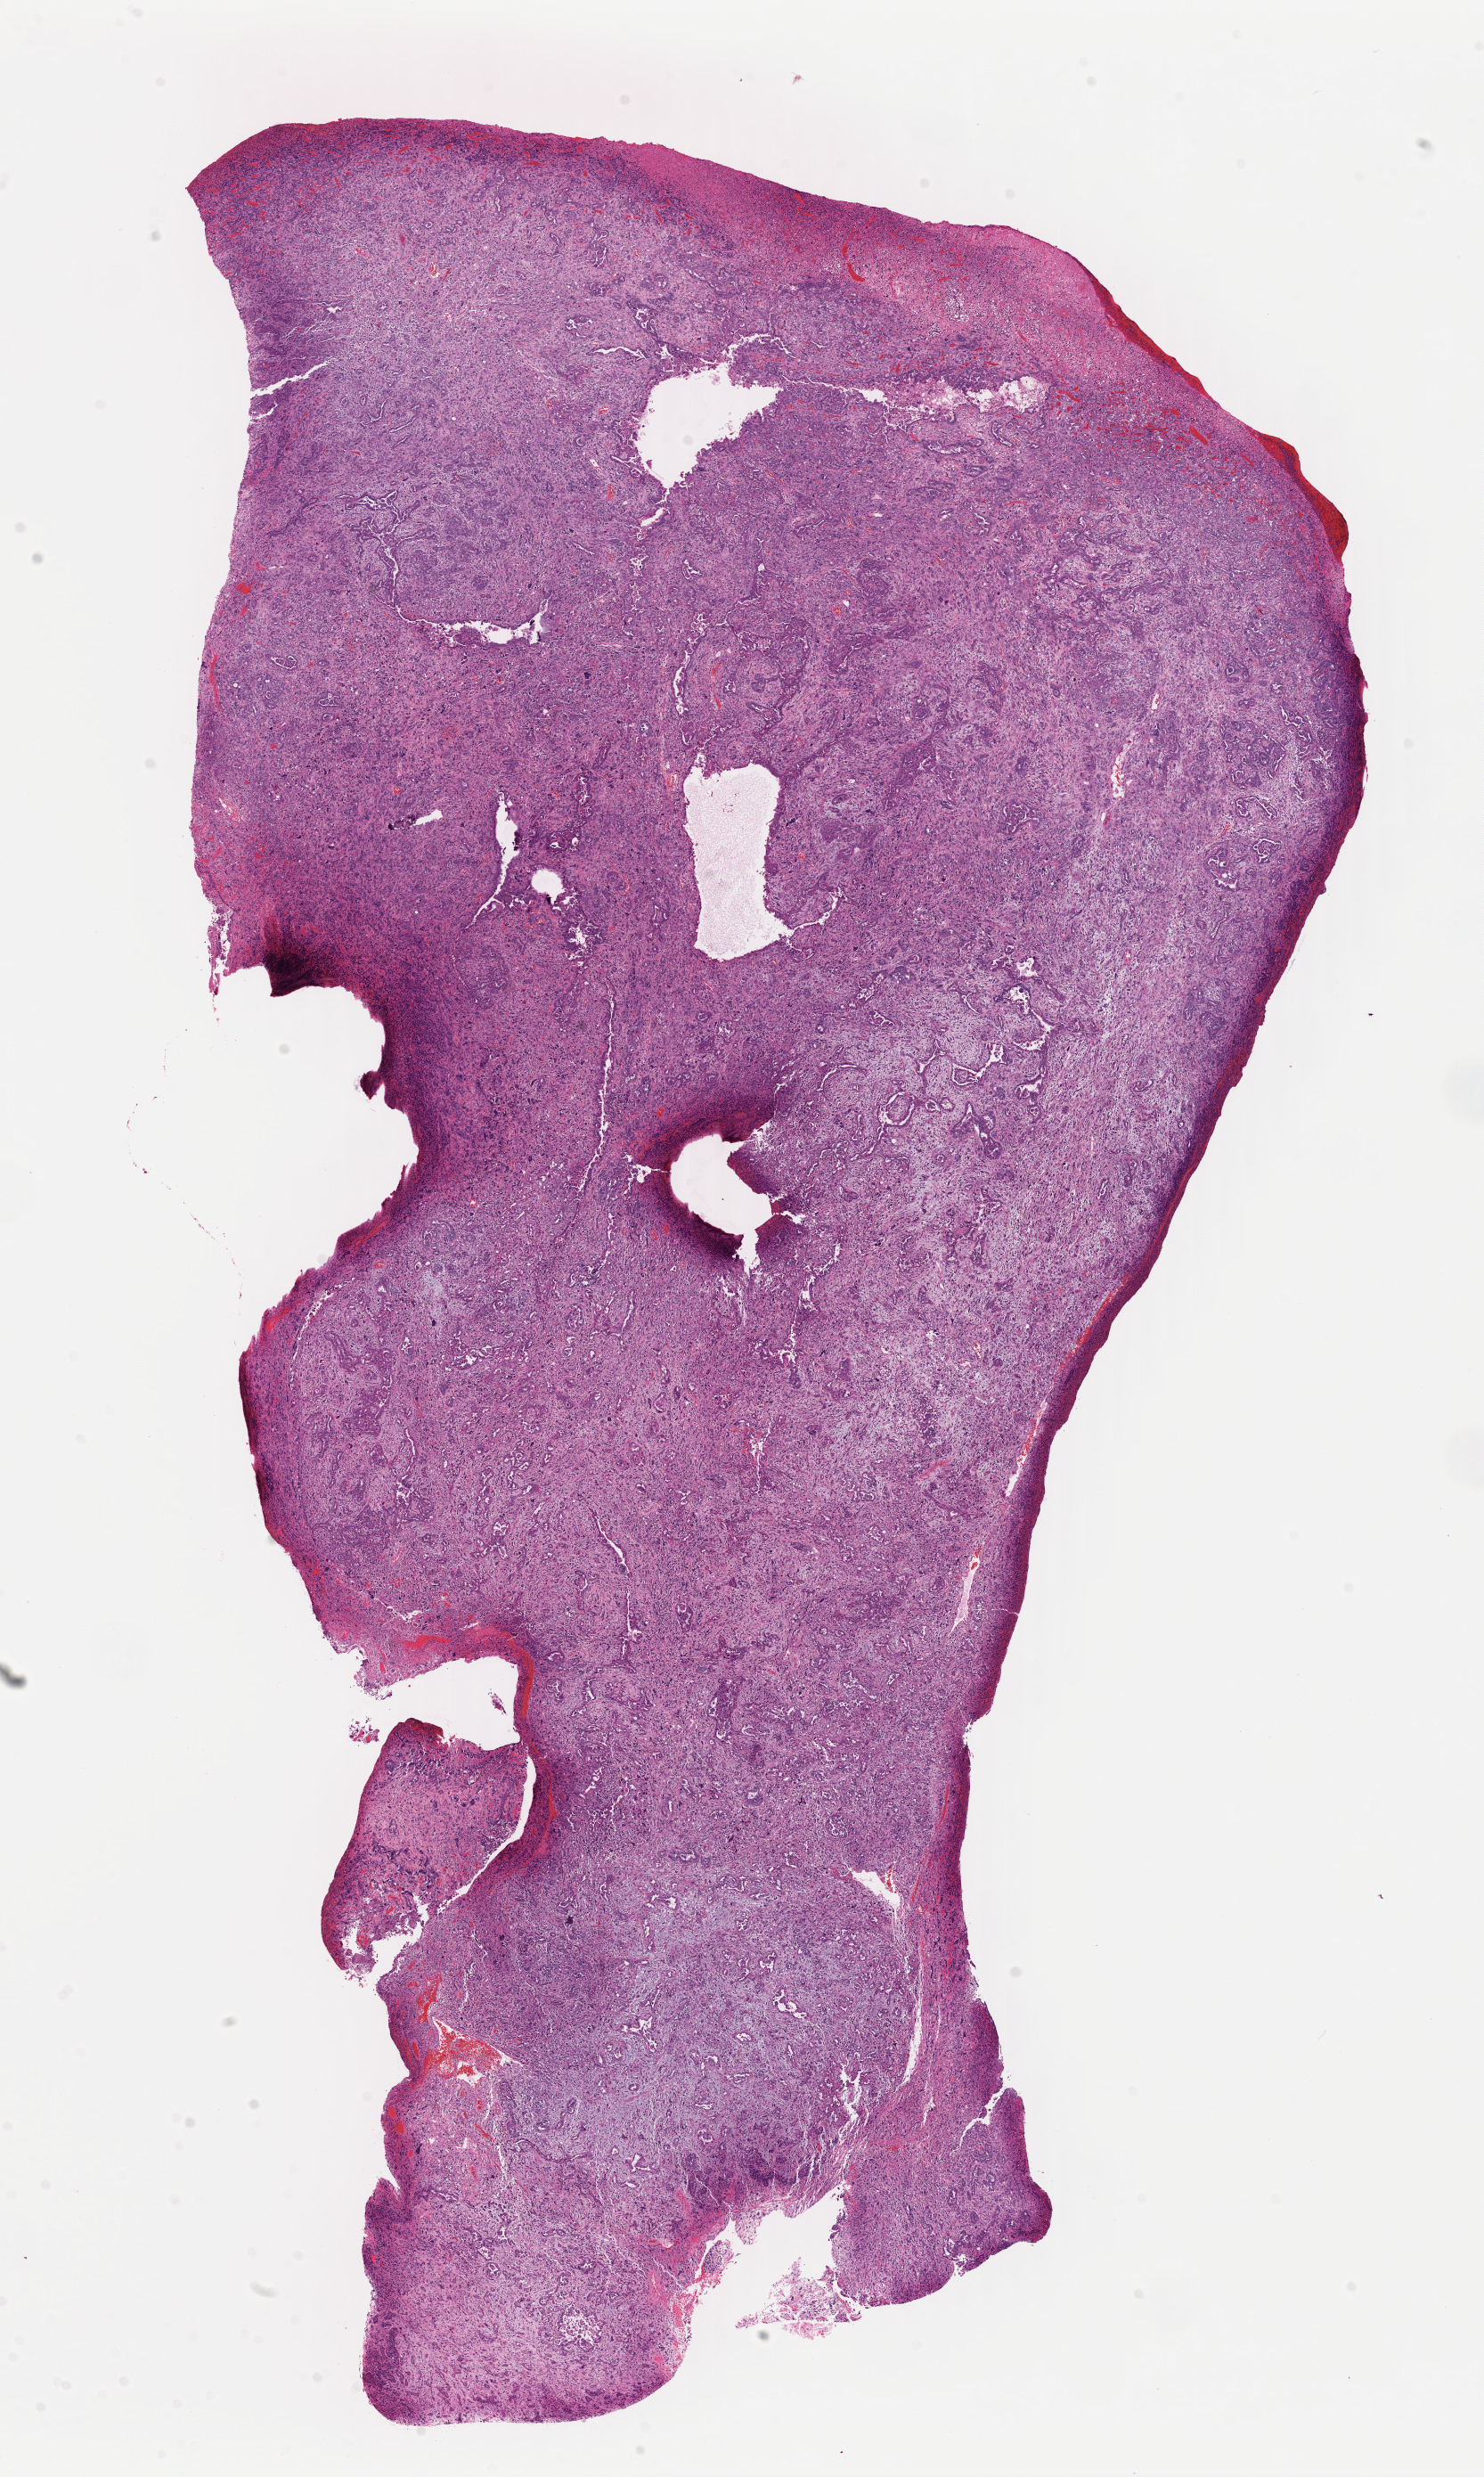
H&E whole-slide image, a low-resolution overview of the entire scanned area, about 13.1 x 21.8 mm (slide scanned at 40x), formalin-fixed paraffin-embedded (FFPE) diagnostic section, sample: primary tumour, uterus. Female, age 67 years at initial diagnosis.
Histologic diagnosis: Mullerian mixed tumor. FIGO stage: IIIC.